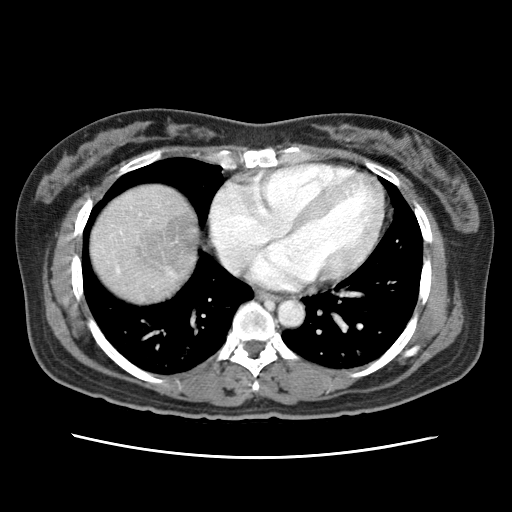
Contrast-enhanced abdominal CT (liver protocol), one axial slice. Slice 67 of 79 in the series (ordered by position). Reconstruction kernel STANDARD. Soft-tissue window (W 400 / L 40 HU). 512 × 512 image matrix. From the clinical record (not read from this slice): diagnosis: hepatocellular carcinoma (patient treated with transarterial chemoembolisation; whether this scan precedes or follows treatment is not stated here); TNM stage (as recorded): Stage-I; Child-Pugh class: A; tumour differentiation: moderately differentiated.
Structures marked on this image (semi-automatically segmented with operator editing):
- abdominal aorta: box from (x=277, y=299) to (x=303, y=327) px
- liver parenchyma outside the tumour (the mass and vessels are separate outlines, so this box may not span the whole liver): (x=90, y=184)–(x=196, y=302)
- liver vessels: (x=117, y=269)–(x=119, y=272)